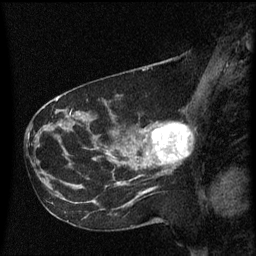
Breast MRI (dynamic contrast-enhanced), one sagittal slice; slice 27 of 60 in the series (ordered by position); dynamic contrast-enhanced series, image 2 of 3 at this slice position (ordered by acquisition); 1.5 T; TE 4.2 ms, TR 8.4 ms; 2 mm slice thickness; 256 × 256 image matrix, field of view 200 × 200 mm. Female patient, age 41 years. From the clinical record (not read from this slice): setting: breast cancer imaged before/during neoadjuvant chemotherapy; receptor status: triple-negative.
Structures marked on this image (semi-automatic segmentation, software-assisted and operator-edited):
- analysis volume of interest (the breast-tissue region the enhancement analysis was run in; not a lesion): bounding box [x1, y1, x2, y2] px = [138, 112, 190, 177]
- tumour enhancement mask (voxels above the 70 % enhancement threshold inside the analysis volume of interest): [151, 124, 189, 163]